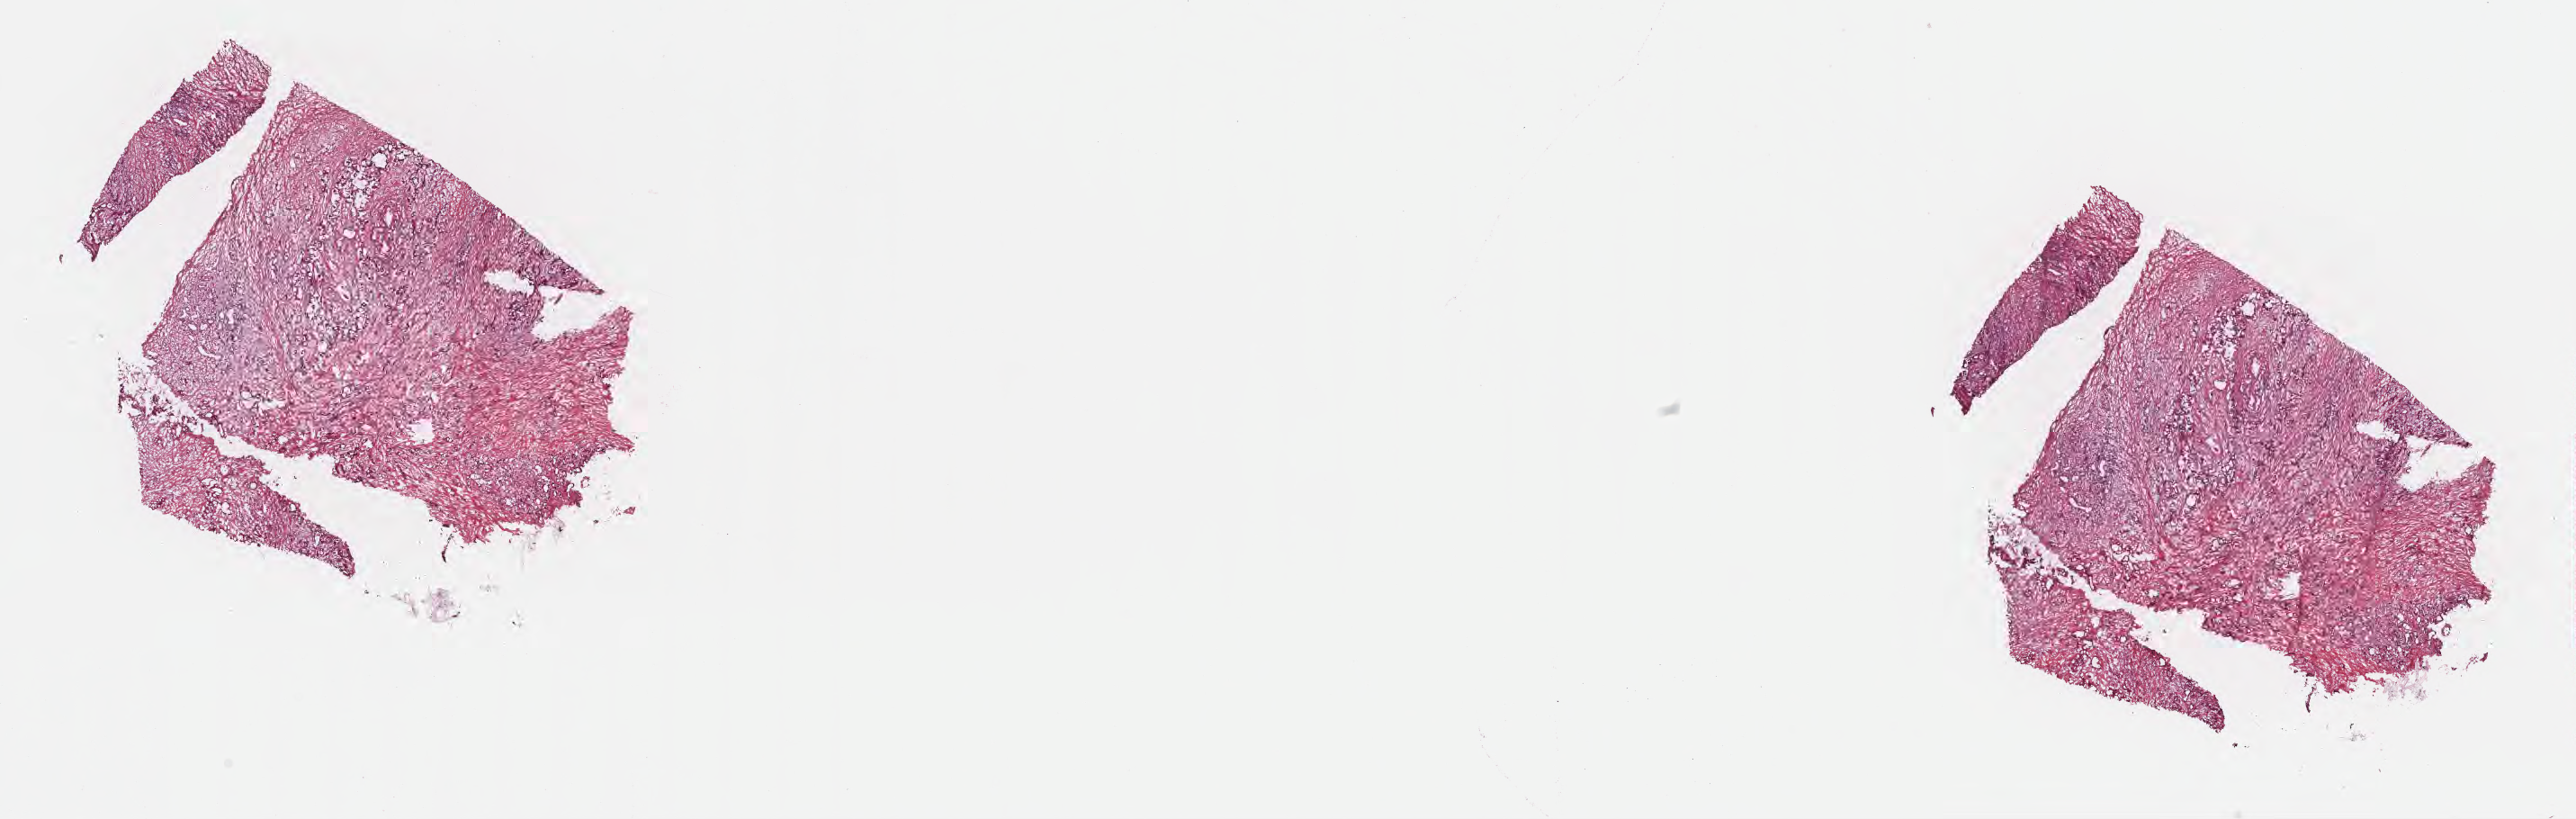
Whole-slide image, hematoxylin and eosin (H&E) stain — whole scanned area (about 23.2 x 7.4 mm) shown as a low-resolution overview, cryosection, primary tumor, site: head of pancreas. Female patient; age at initial diagnosis 77 years. Tumor grade: G2 (moderately differentiated). Composition of this section per pathologist review: tumor cells 20%, tumor nuclei 40%, stromal cells 80%, necrosis 0%, normal cells 0%. Inflammatory infiltration, as recorded: lymphocyte infiltration 0%, monocyte infiltration 0%, neutrophil infiltration 0%.
Section: bottom of the tissue portion. Histologic diagnosis: Infiltrating duct carcinoma, NOS. AJCC pathologic stage: Stage III.